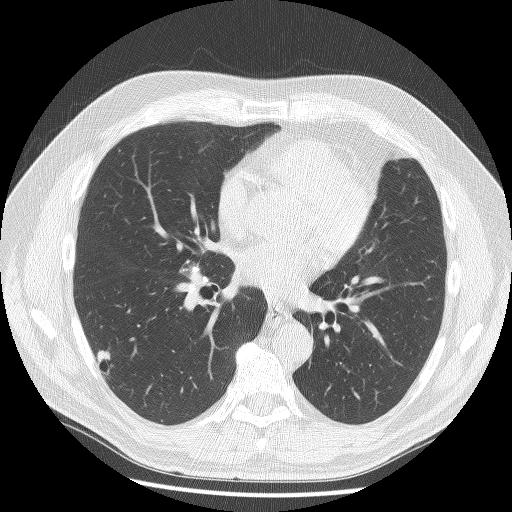
Chest CT (low-dose screening protocol), one axial image; baseline screening round; lung window (W 1500 / L -600 HU); 2.5 mm slice thickness; 120 kVp; slice 92 of 179 in the series. Male, age 61 years at enrolment.
• Expert reader's lesion annotation, bounding box (x1, y1, x2, y2) in pixels: (80, 339, 132, 391).
• Reader record for this screening exam (exam-level; its link to the box is not recorded): non-calcified nodule or mass ≥4 mm, right lower lobe, 10 × 8 mm, spiculated (stellate) margins, soft tissue attenuation.
• Official screen result: positive, change unspecified: nodule(s) >= 4 mm or enlarging nodule(s), mass(es), or other non-specific abnormalities suspicious for lung cancer.
• Lung cancer was diagnosed 407 days after this screen: adenosquamous carcinoma, right lower lobe, poorly differentiated (G3), stage IV (AJCC 6th edition), 45 mm at pathology.